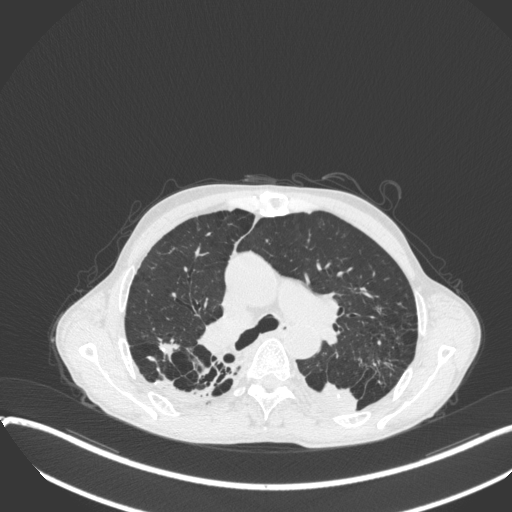
Chest CT, one axial slice; slice 253 of 400 in the series (ordered by position); reconstruction kernel B31f; lung window (W 1500 / L -600 HU); 1 mm slice thickness; 512 × 512 image matrix. Male patient, age 57 years. From the clinical record (not read from this slice): clinical TNM (as recorded): T4 N0 M0.
Structures marked on this image (rectangle marked by the reading radiologist):
- lung tumour (recorded histology: squamous cell carcinoma): box from (x=297, y=375) to (x=360, y=418) px